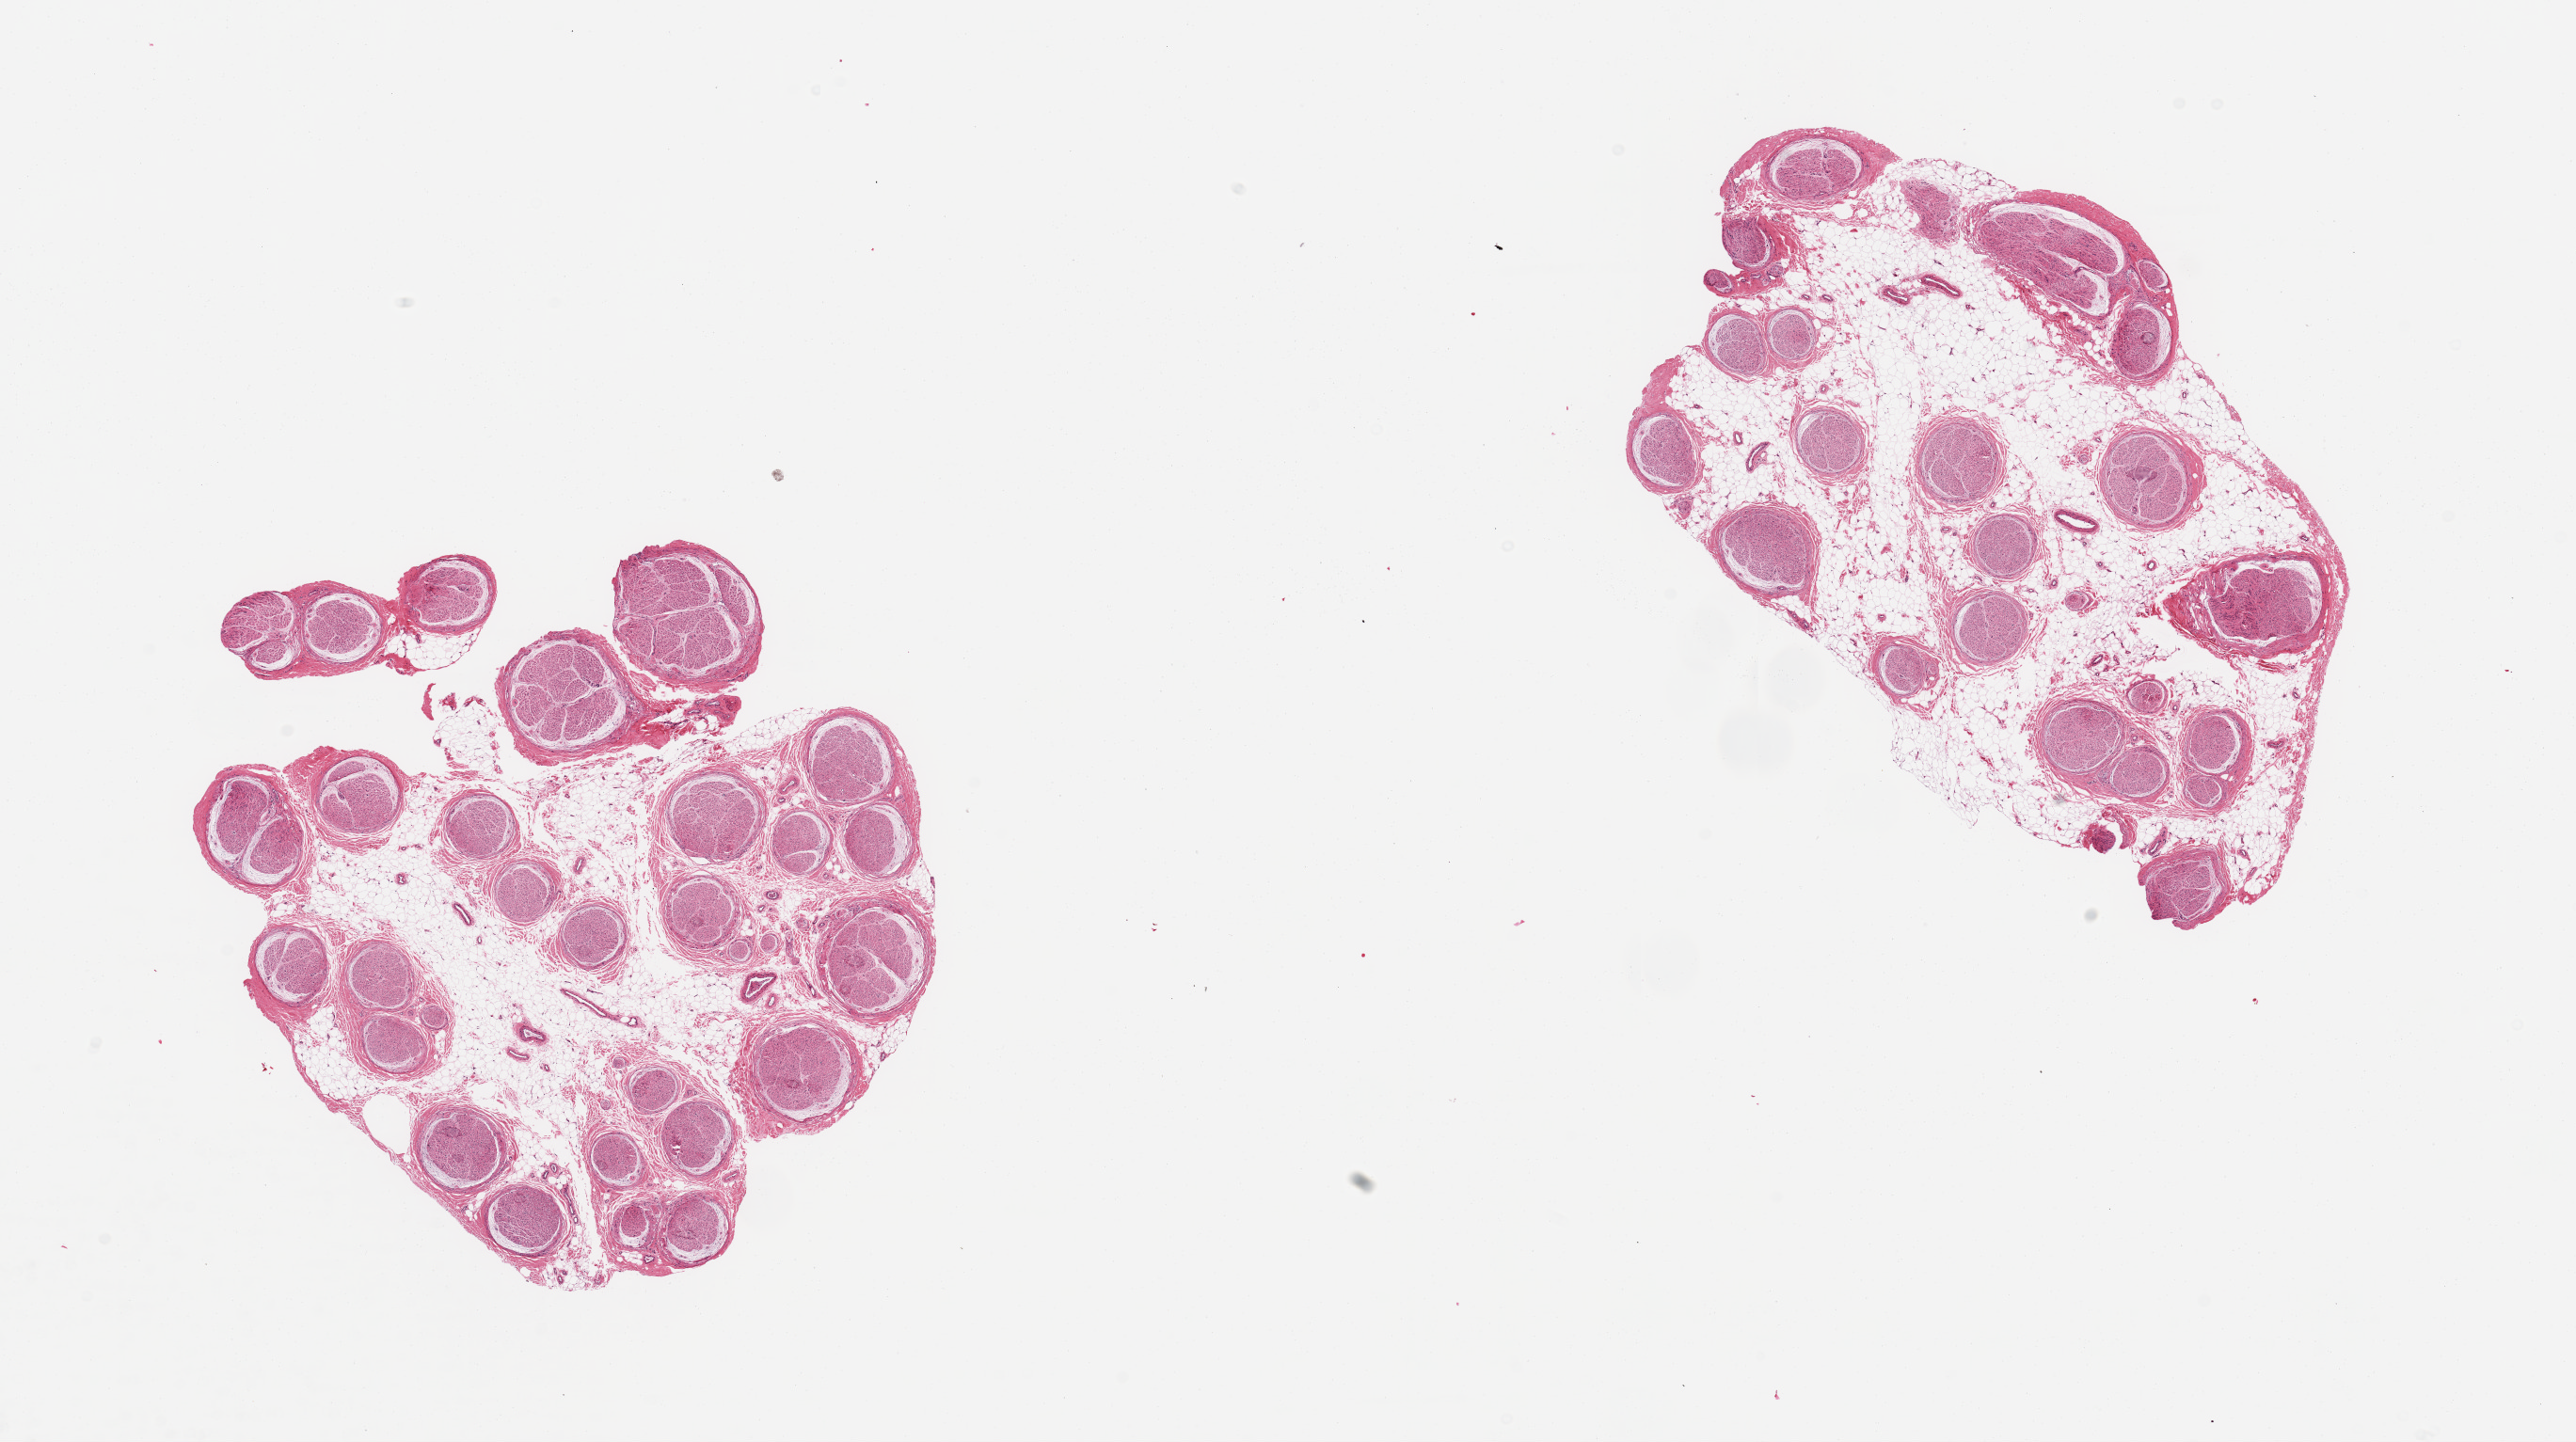
Hematoxylin and eosin (H&E) whole-slide image, brightfield — low-resolution overview of the scanned area, about 21.7 x 12.1 mm; PAXgene-fixed, paraffin-embedded tissue; section of tibial nerve (target tissue); tissue donor sample. Male donor.
Review note (as recorded): 2 pieces; prominent 40% internal fat content.